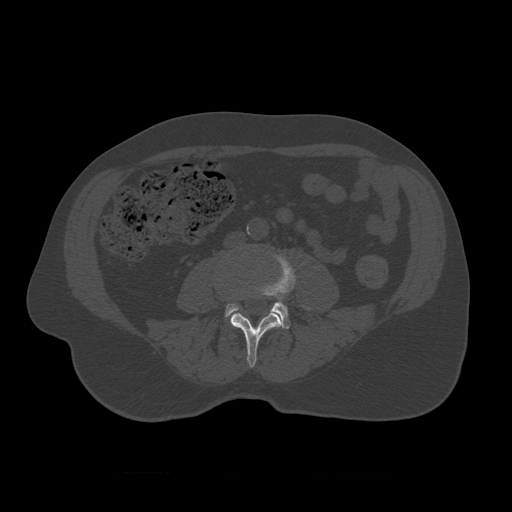
CT including the spine, one axial slice; position 290 of 450 along the scan axis; 120 kVp; bone window (W 1800 / L 400 HU); 512 × 512 image matrix. Patient age 75 years. From the clinical record (not read from this slice): primary cancer: prostate.
Annotated regions visible in this slice (semi-automatically segmented with operator editing):
- L3 vertebra: bounding box (x1, y1, x2, y2) in pixels: (230, 292, 282, 368)
- L4 vertebra: (225, 250, 311, 329)